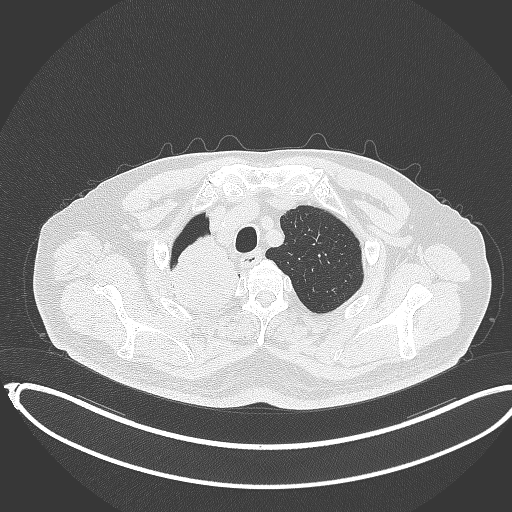
Chest CT, one axial slice. Slice 319 of 403 in the series (ordered by position). Reconstruction kernel B70f. 120 kVp. Lung window (W 1500 / L -600 HU). 1 mm slice thickness. 512 × 512 image matrix, field of view 436 × 436 mm. Patient: male, 68 years. Case-level facts recorded for this patient, not image findings: clinical TNM (as recorded): T2a N0 M0.
Structures marked on this image (rectangle marked by the reading radiologist):
- lung tumour (recorded histology: adenocarcinoma): bounding box [x1, y1, x2, y2] px = [169, 236, 244, 319]